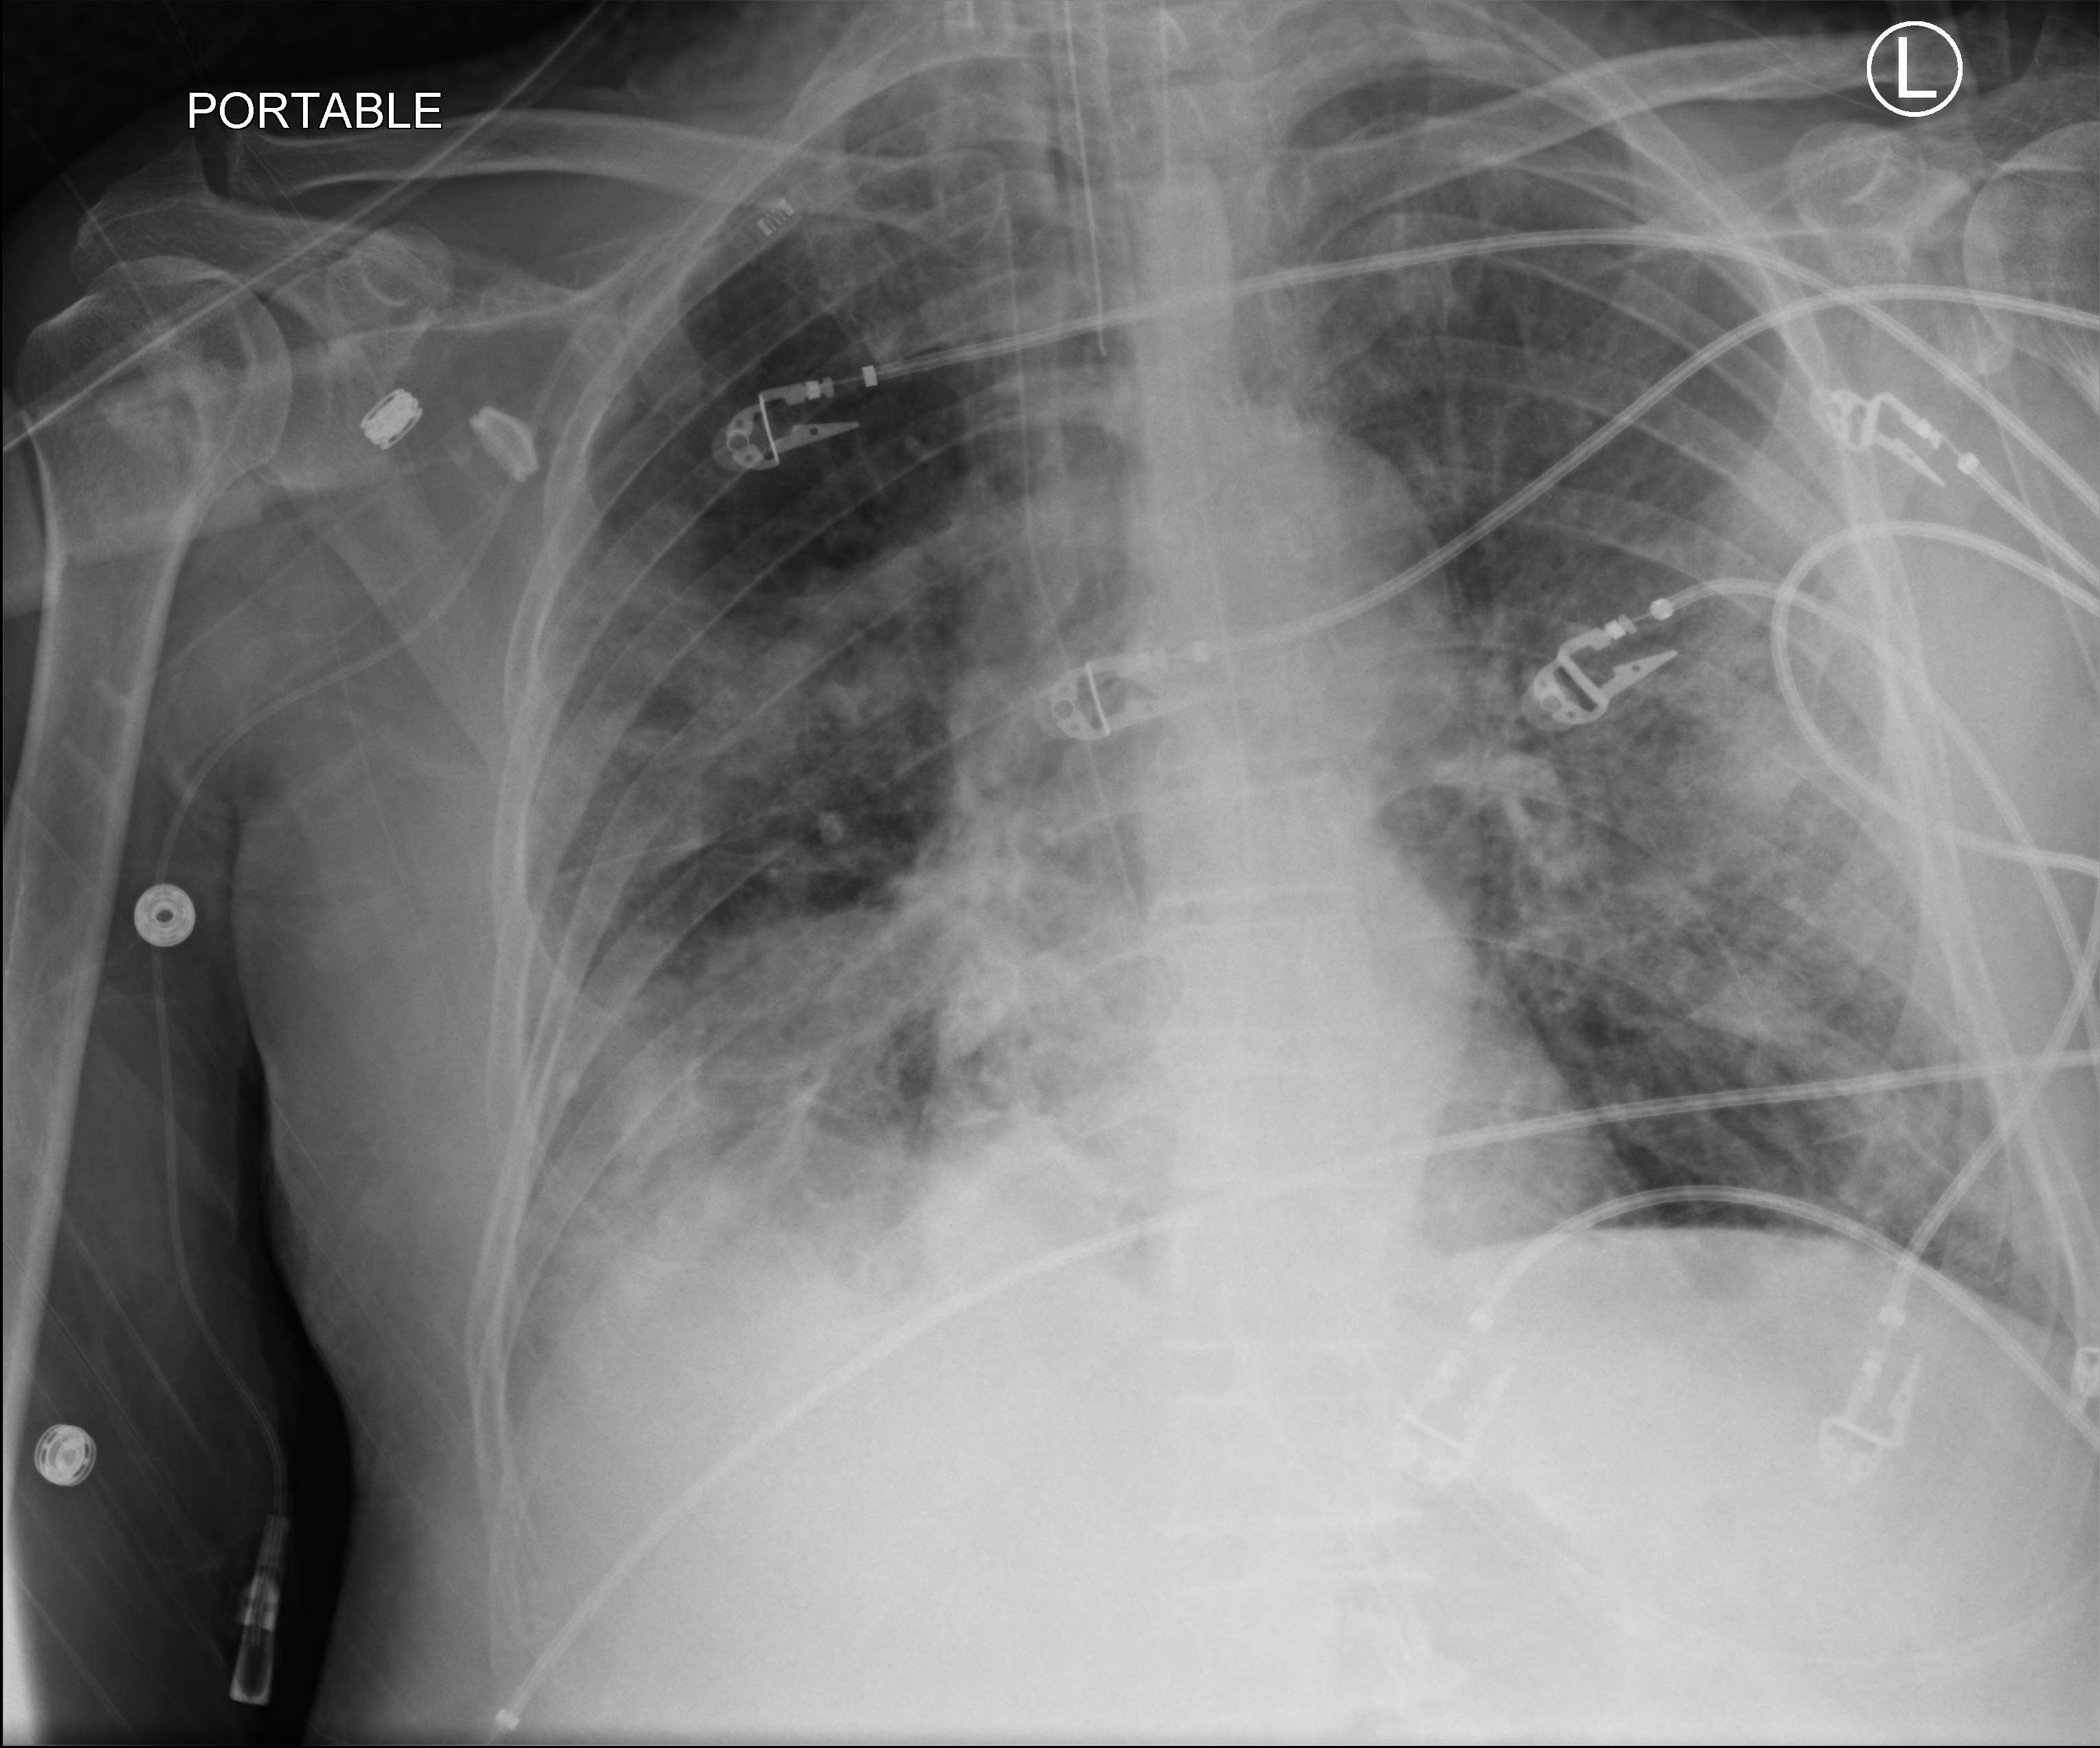
Portable chest radiograph; anteroposterior (AP) projection. Patient hospitalised with COVID-19; male, aged 75–90 years.
Hospital-stay facts (about this admission, not read from this image; timing relative to this image not recorded):
- admitted to intensive care during this hospital stay: yes